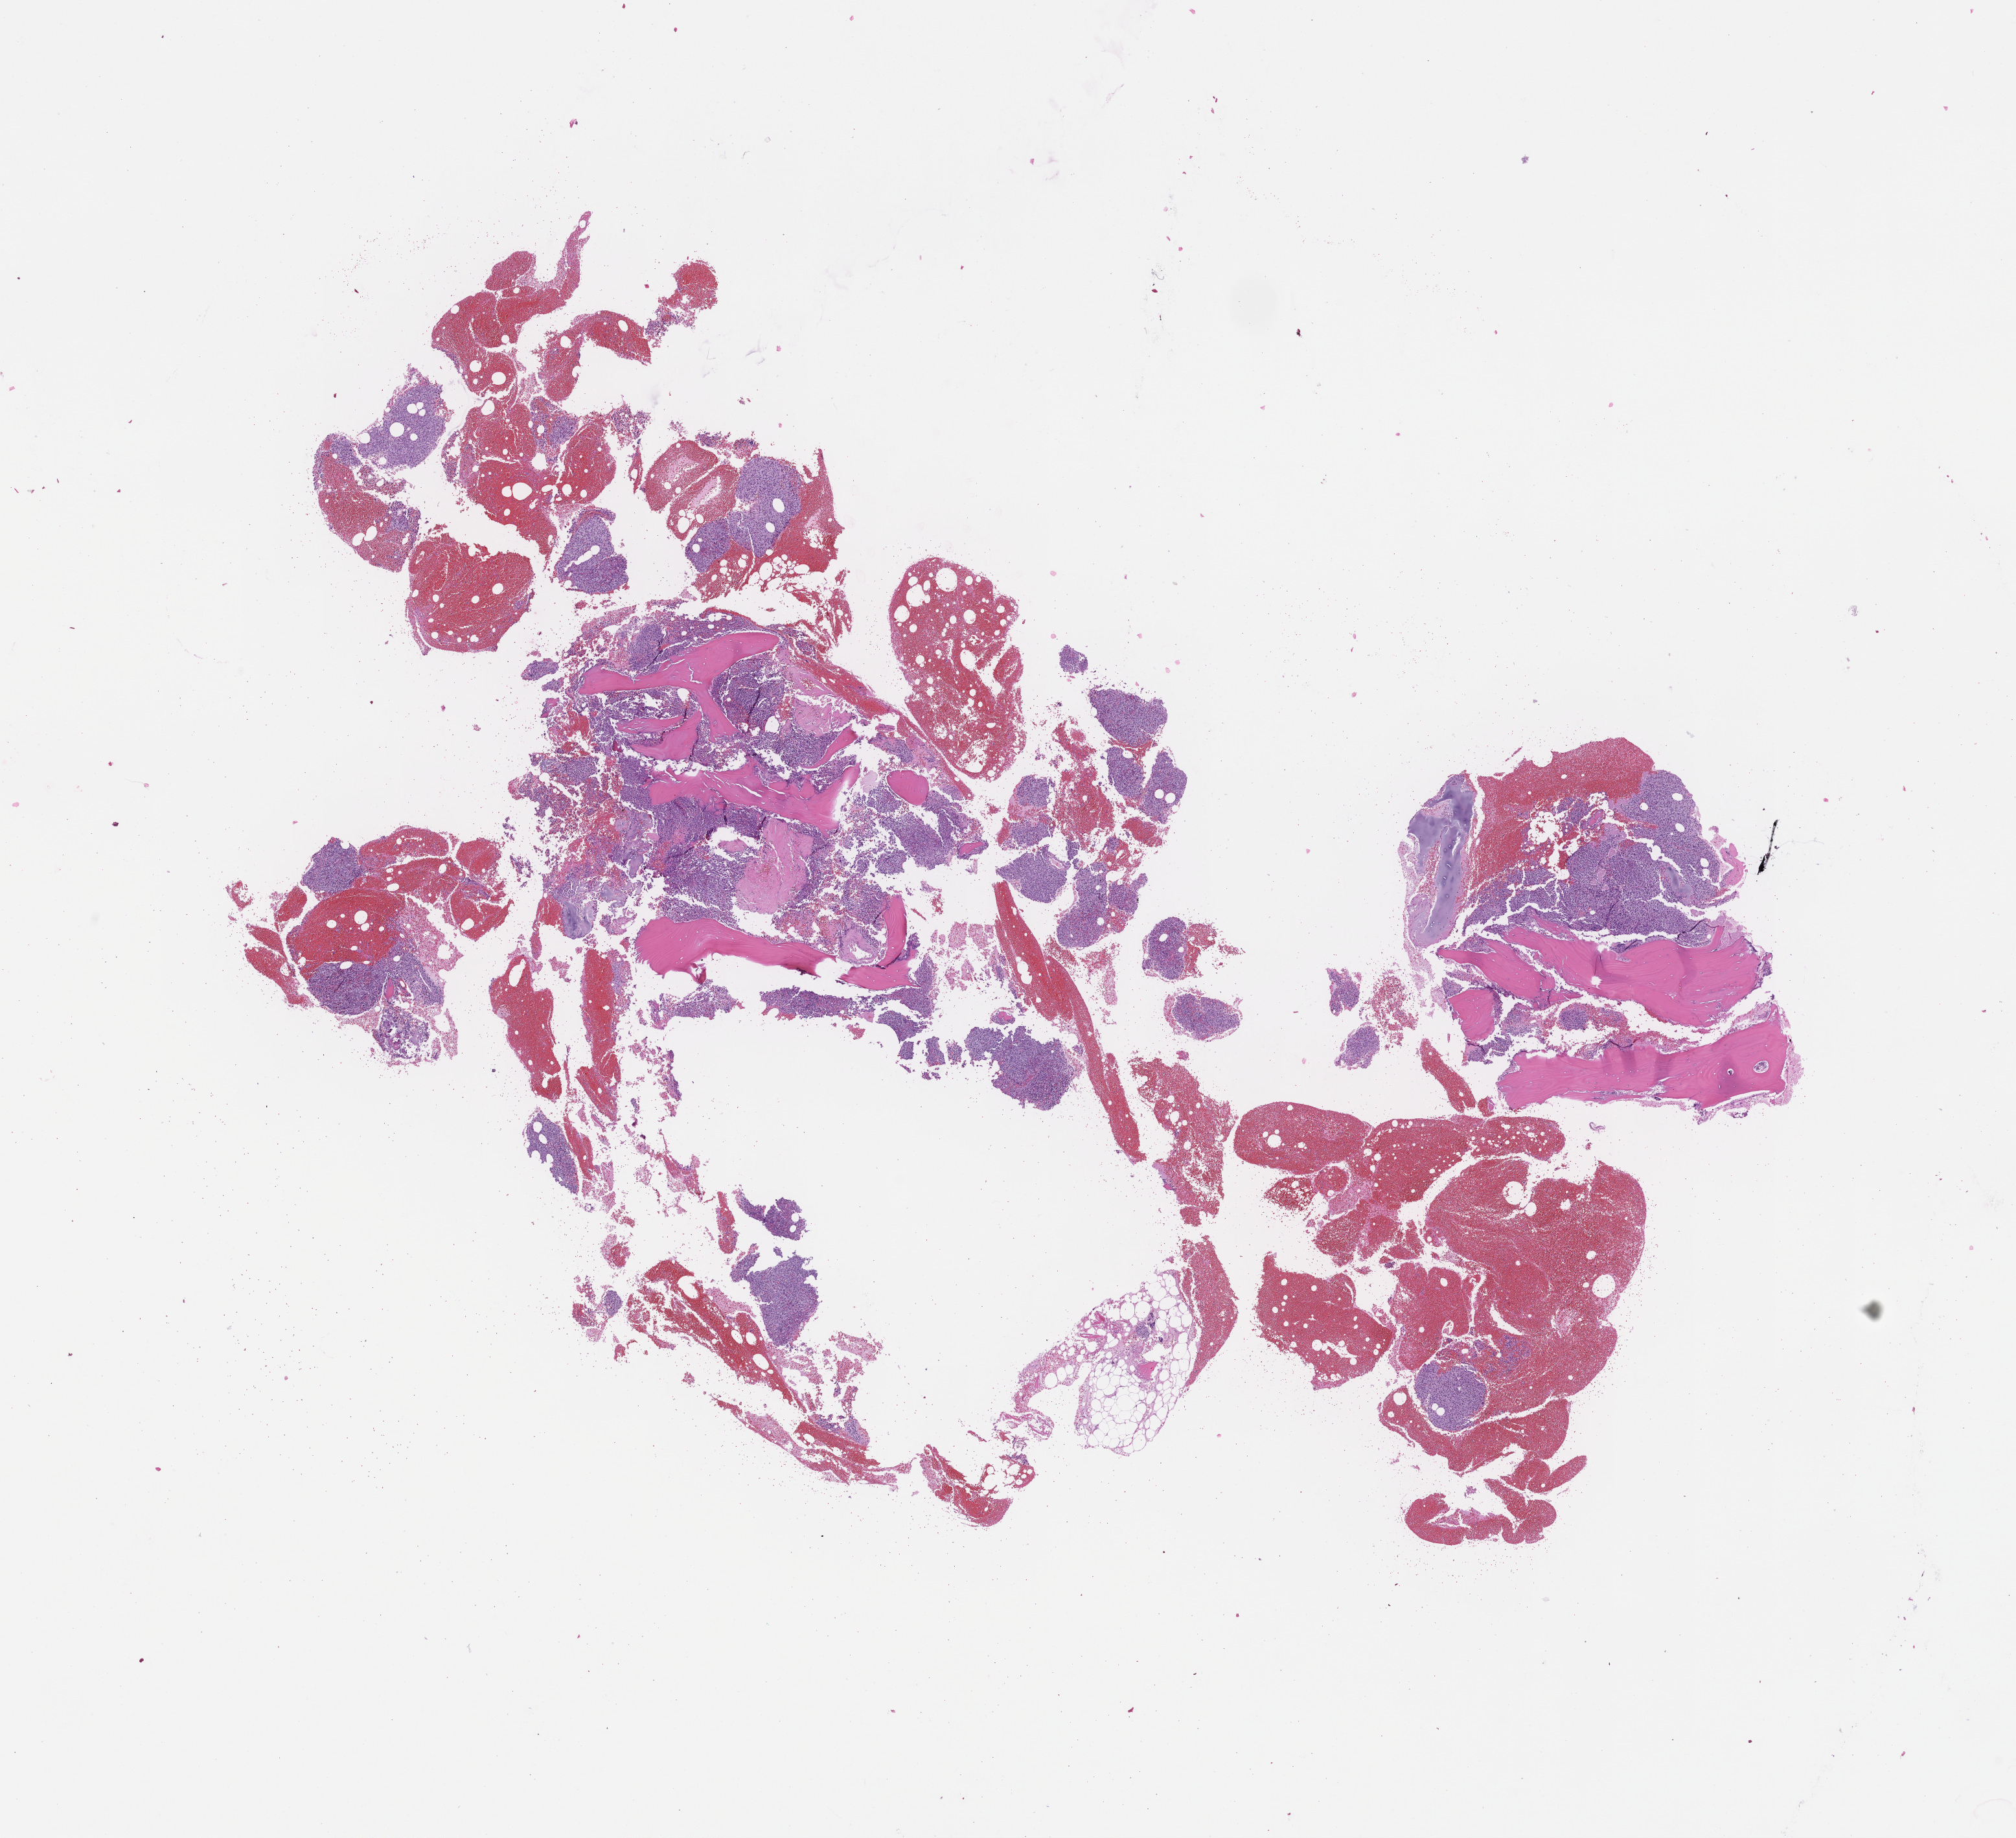
Whole-slide image, haematoxylin and eosin stain — a low-resolution overview of the entire scanned area, about 12.6 x 11.5 mm, formalin-fixed paraffin-embedded section, site: bone marrow, specimen time point: archival tissue. Male patient.
This section: primary tumor. Diagnosis: Plasma Cell Myeloma.